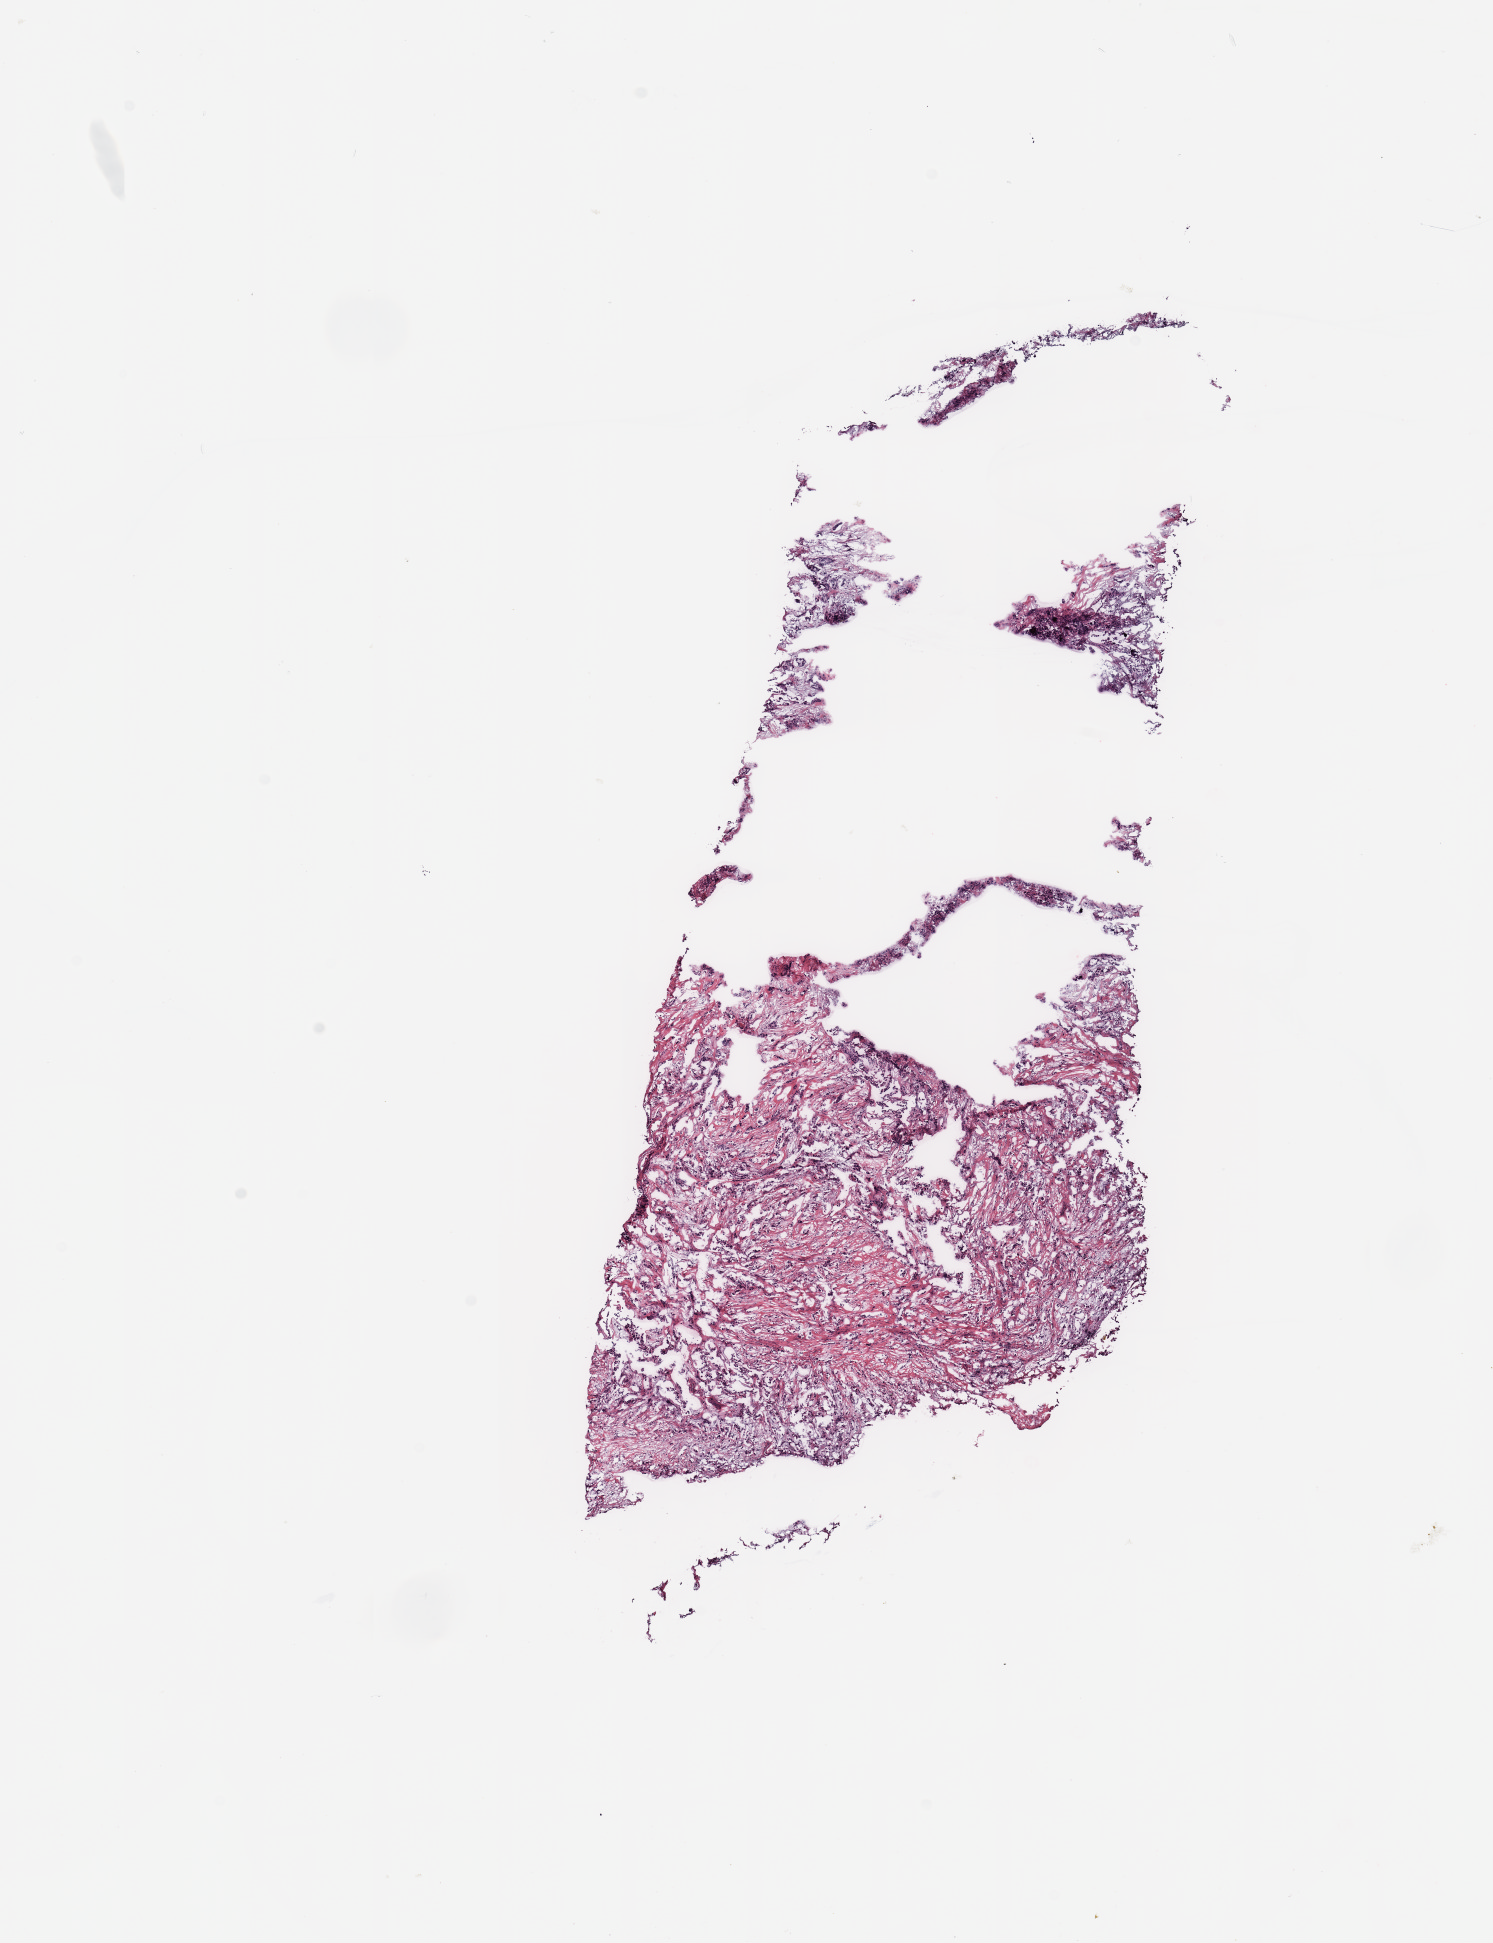
Whole-slide histology image, H&E, a low-resolution overview of the entire scanned area, about 11.8 x 15.4 mm (acquisition: 20x scan). Tumour tissue sample, breast. Female, 71 y/o.
AJCC pathologic stage: IIA. Diagnosis: Infiltrating duct carcinoma, NOS.